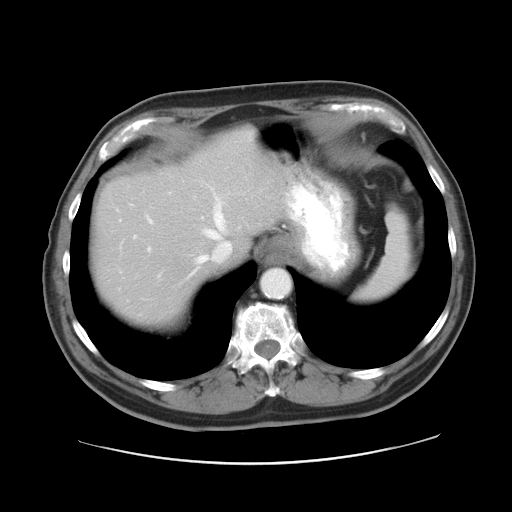
Contrast-enhanced abdominal CT, one axial slice; slice 23 of 28 in the series (ordered by position); reconstruction kernel STANDARD; 120 kVp; intravenous contrast given; soft-tissue window (W 400 / L 40 HU); 7.5 mm slice thickness; 512 × 512 image matrix, field of view 402 × 402 mm. Male patient, age 74 years. From the clinical record (not read from this slice): diagnosis: colorectal cancer liver metastases, imaged before liver resection; multiple liver metastases: no; largest metastasis: 5 cm; disease in both lobes: no.
Structures marked on this image (manually delineated by an expert):
- hepatic veins: bounding box (x1, y1, x2, y2) in pixels: (133, 194, 231, 276)
- liver: (96, 134, 280, 322)
- planned liver remnant (the part of the liver to remain after resection): (96, 182, 214, 323)